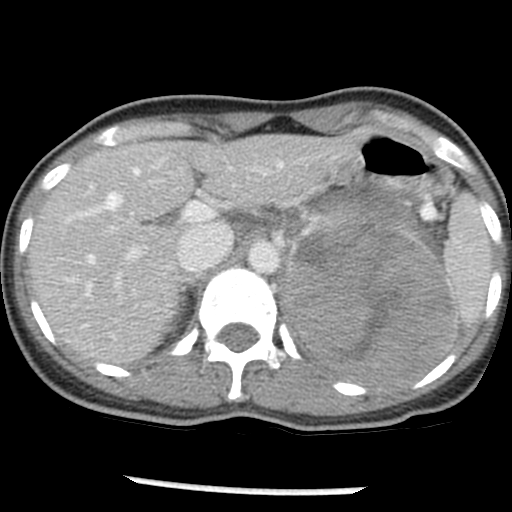
Contrast-enhanced abdominal CT, one axial slice; position 33 of 54 along the scan axis; reconstruction kernel STANDARD; intravenous contrast given; soft-tissue window (W 400 / L 40 HU); 512 × 512 image matrix, field of view 240 × 240 mm. Female patient, age 33 years. Case-level facts recorded for this patient, not image findings: diagnosis: adrenocortical carcinoma; tumour side: left adrenal; tumour size at pathology: 11 cm; Ki-67 index: 20 %; stage (as recorded): 2.
Annotated regions visible in this slice (semi-automatically segmented with operator editing):
- mass: bounding box (x1, y1, x2, y2) in pixels: (277, 192, 455, 380)